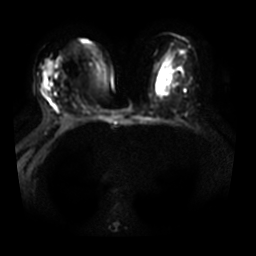
Breast MRI, one axial slice. Position 17 of 31 along the scan axis. Diffusion-weighted series; image 2 of 4 stored at this slice position (different b-values; order by instance number). 3 T. 256 × 256 image matrix. Female patient.
Outlined on this slice (manually delineated by an expert):
- tumour on diffusion-weighted imaging: bounding box [x1, y1, x2, y2] px = [42, 61, 53, 78]